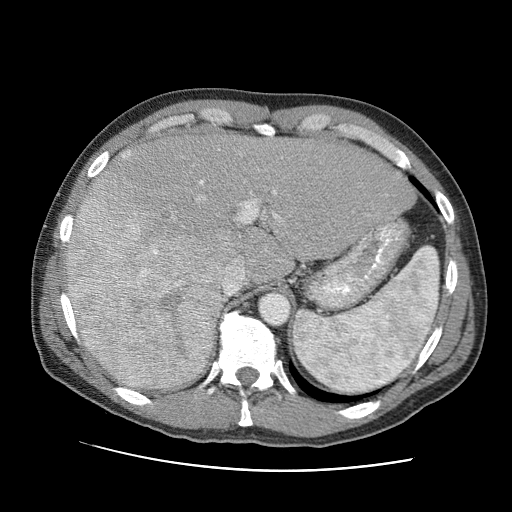
Contrast-enhanced abdominal CT (liver protocol), one axial slice. Slice 67 of 95 in the series (ordered by position). Reconstruction kernel STANDARD. 120 kVp. One of 2 acquisitions stored at this slice position. Soft-tissue window (W 400 / L 40 HU). 512 × 512 image matrix, field of view 360 × 360 mm. From the clinical record (not read from this slice): diagnosis: hepatocellular carcinoma (patient treated with transarterial chemoembolisation; whether this scan precedes or follows treatment is not stated here); TNM stage (as recorded): Stage-IVA; Child-Pugh class: A.
Annotated regions visible in this slice (semi-automatically segmented with operator editing):
- liver parenchyma outside the tumour (the mass and vessels are separate outlines, so this box may not span the whole liver): bounding box <69,132,416,390> (left, top, right, bottom; pixels)
- mass: <63,147,228,391>
- liver vessels: <122,155,279,293>